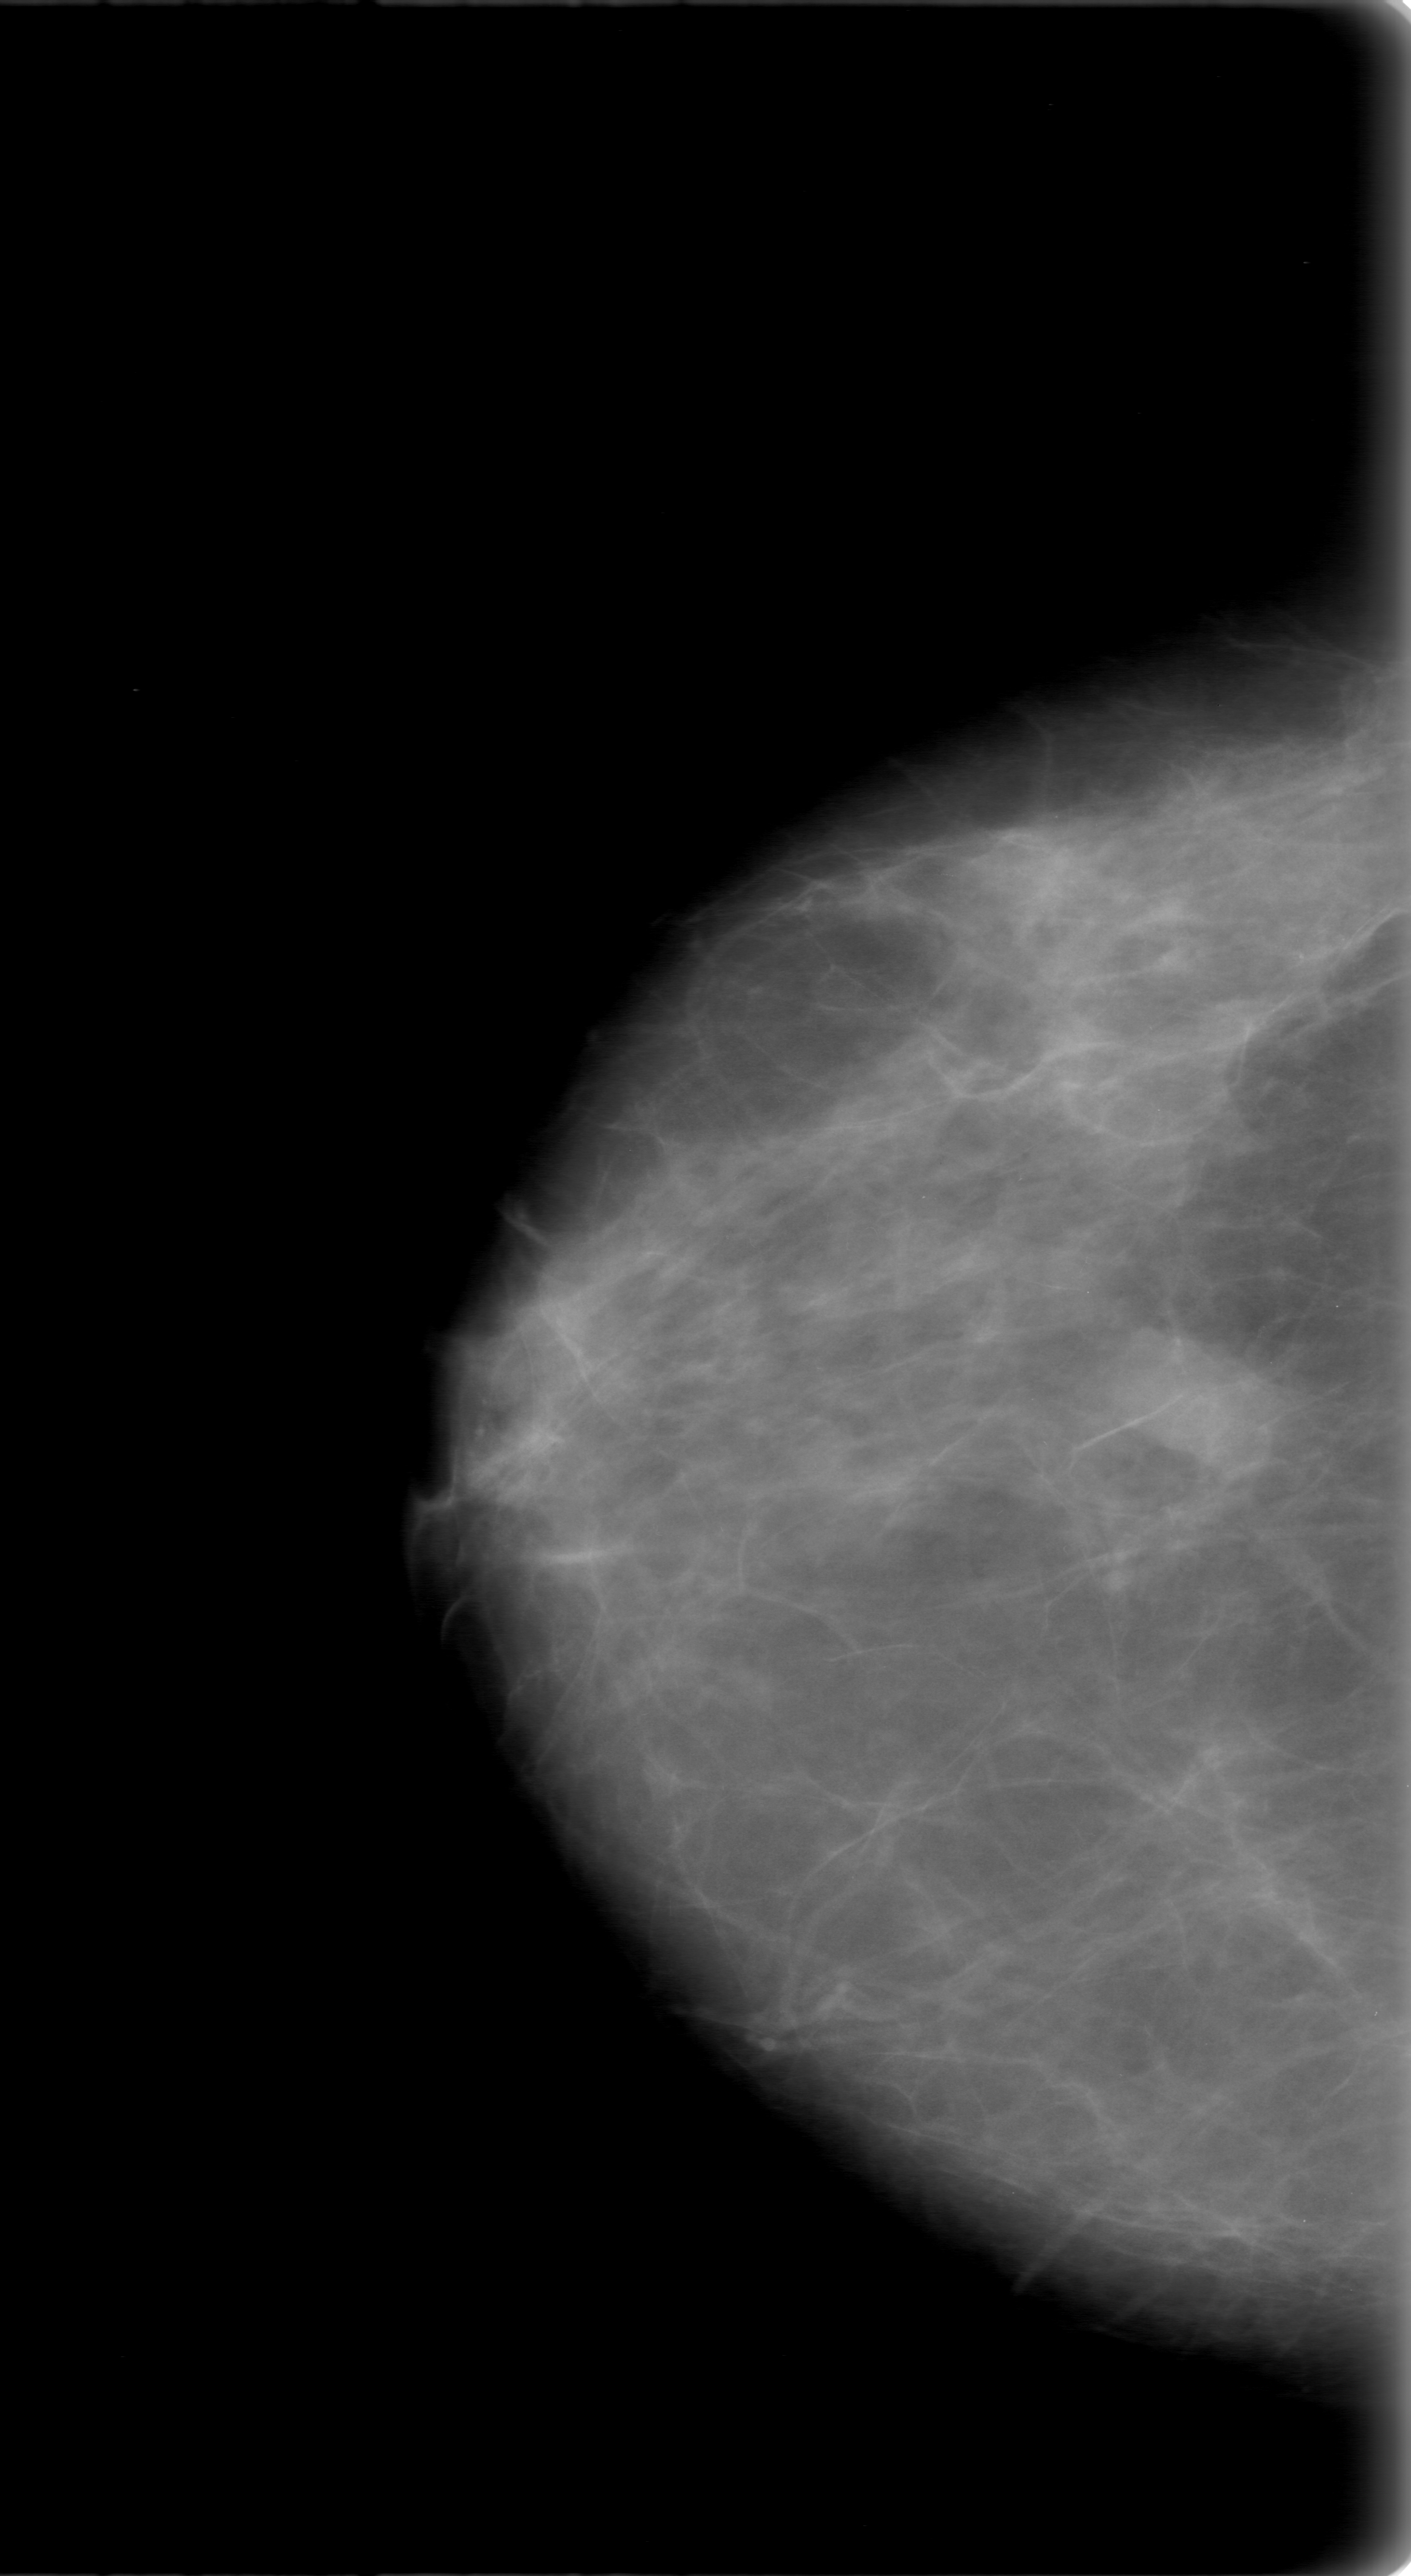
Digitized screen-film mammogram; right breast; craniocaudal (CC) view; breast composition: scattered fibroglandular densities (BI-RADS density category 2 of 4).
Marked abnormality: mass, shape oval, margins obscured; BI-RADS assessment category 0 (incomplete: needs additional imaging); subtlety rating 4 on a 1 (subtle) to 5 (obvious) scale; pathology result (as recorded, not read from the image): benign.